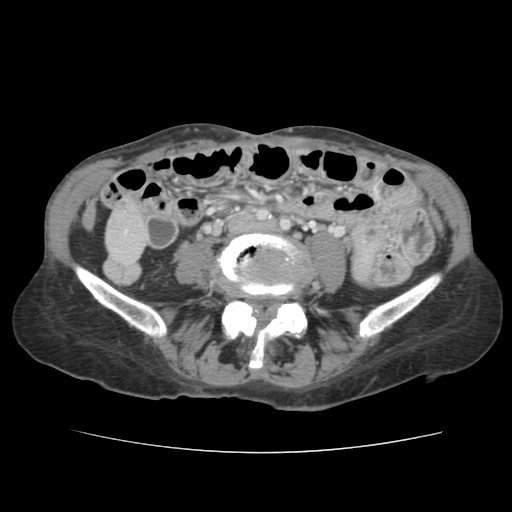
Contrast-enhanced abdominal CT, one axial slice. Position 14 of 136 along the scan axis. 120 kVp. Intravenous contrast given. Soft-tissue window (W 400 / L 40 HU). 512 × 512 image matrix. Female patient, age 77 years. Case-level facts recorded for this patient, not image findings: diagnosis: colorectal cancer liver metastases, imaged before liver resection; multiple liver metastases: yes.
Structures marked on this image (outlined manually by an expert reader):
- liver: bounding box <108,207,145,265> (left, top, right, bottom; pixels)